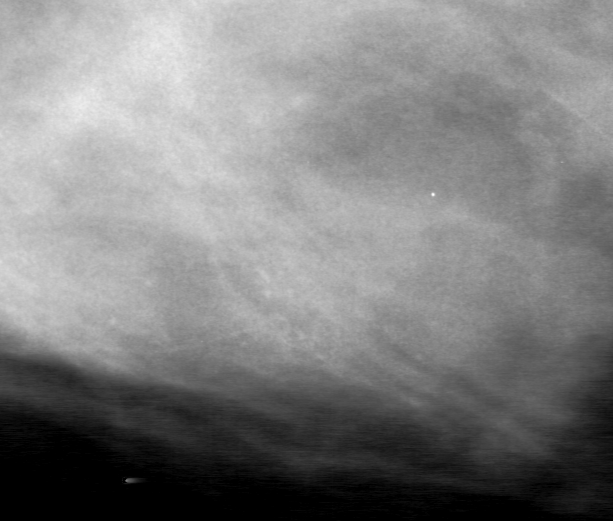
Cropped region of a digitized screen-film mammogram centred on a radiologist-marked abnormality; left breast; MLO view.
Calcifications, morphology amorphous, distribution clustered; BI-RADS assessment category 0 (incomplete: needs additional imaging); pathology result (as recorded, not read from the image): malignant.